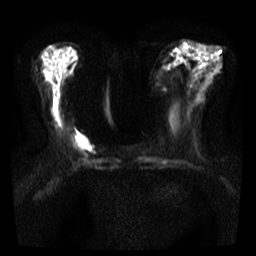
Breast MRI, one axial slice; slice 13 of 35 in the series (ordered by position); diffusion-weighted series; image 2 of 4 stored at this slice position (different b-values; order by instance number); 3 T; 5 mm slice thickness; 256 × 256 image matrix. Female patient.
Structures marked on this image (outlined manually by an expert reader):
- tumour on diffusion-weighted imaging: bounding box (x1, y1, x2, y2) in pixels: (71, 132, 89, 152)